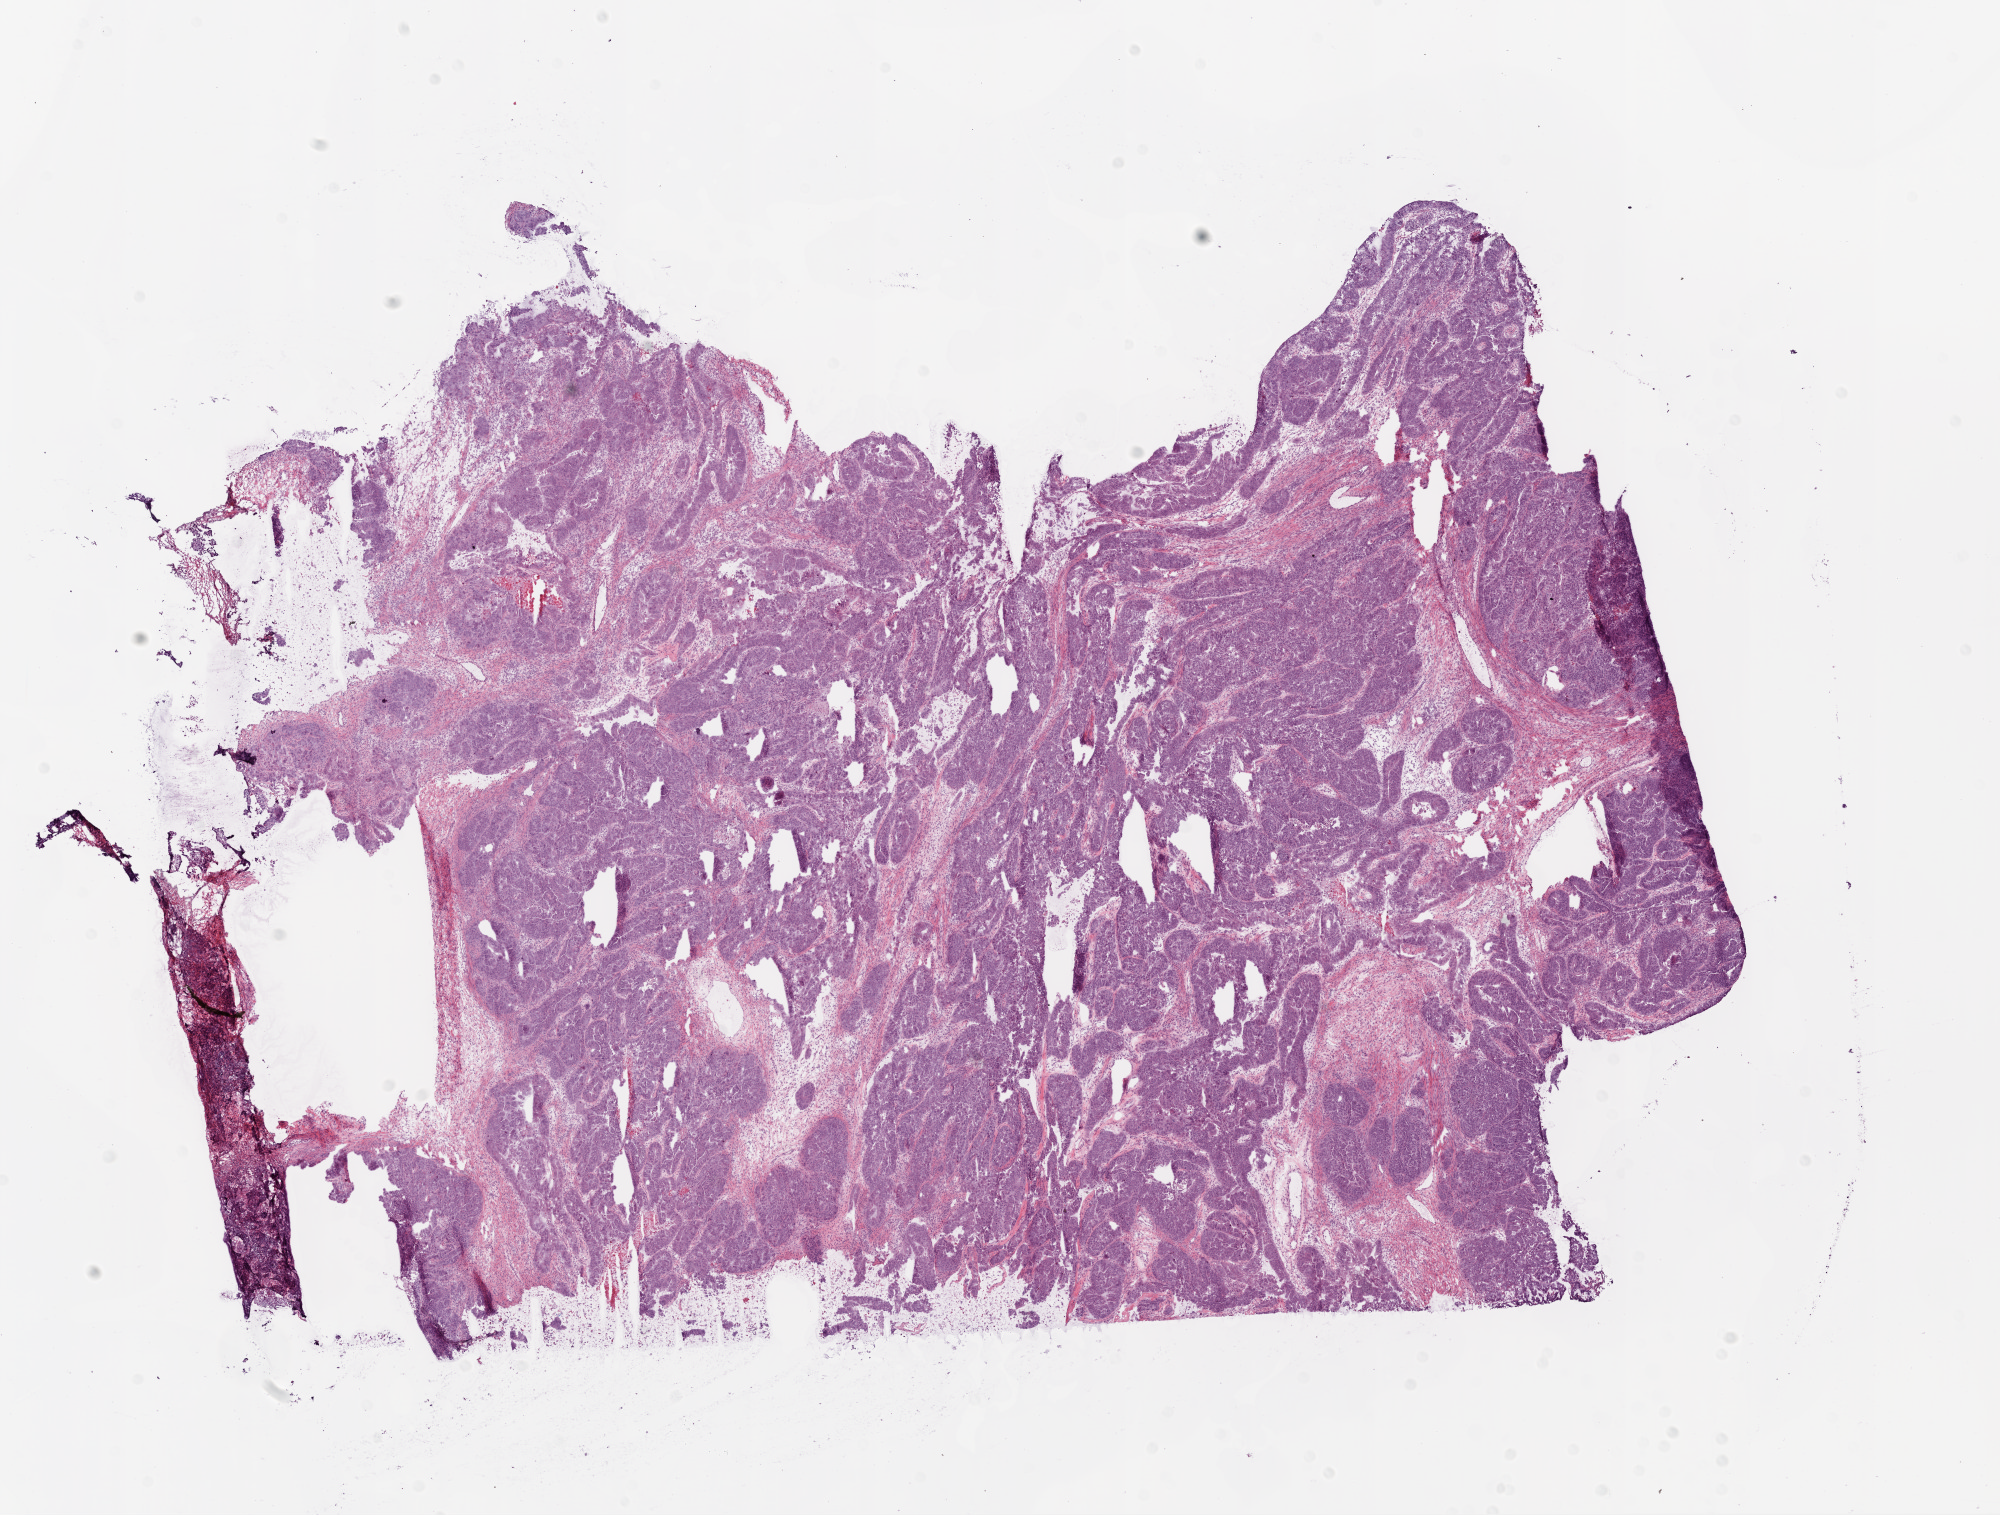
H&E-stained whole-slide image — low-resolution overview of the scanned area, about 16.0 x 12.2 mm; frozen section; primary tumour sample from the ovary. Patient: female, age at initial diagnosis 43 years. Histologic grade: G3 (poorly differentiated). Composition of this section per pathologist review: tumour cells 83%, tumour nuclei 90%, normal cells 0%, stromal cells 15%, necrosis 2%. Infiltration values recorded for this section: lymphocyte infiltration 3%.
Histologic diagnosis: Serous cystadenocarcinoma, NOS. FIGO stage: IIIC.